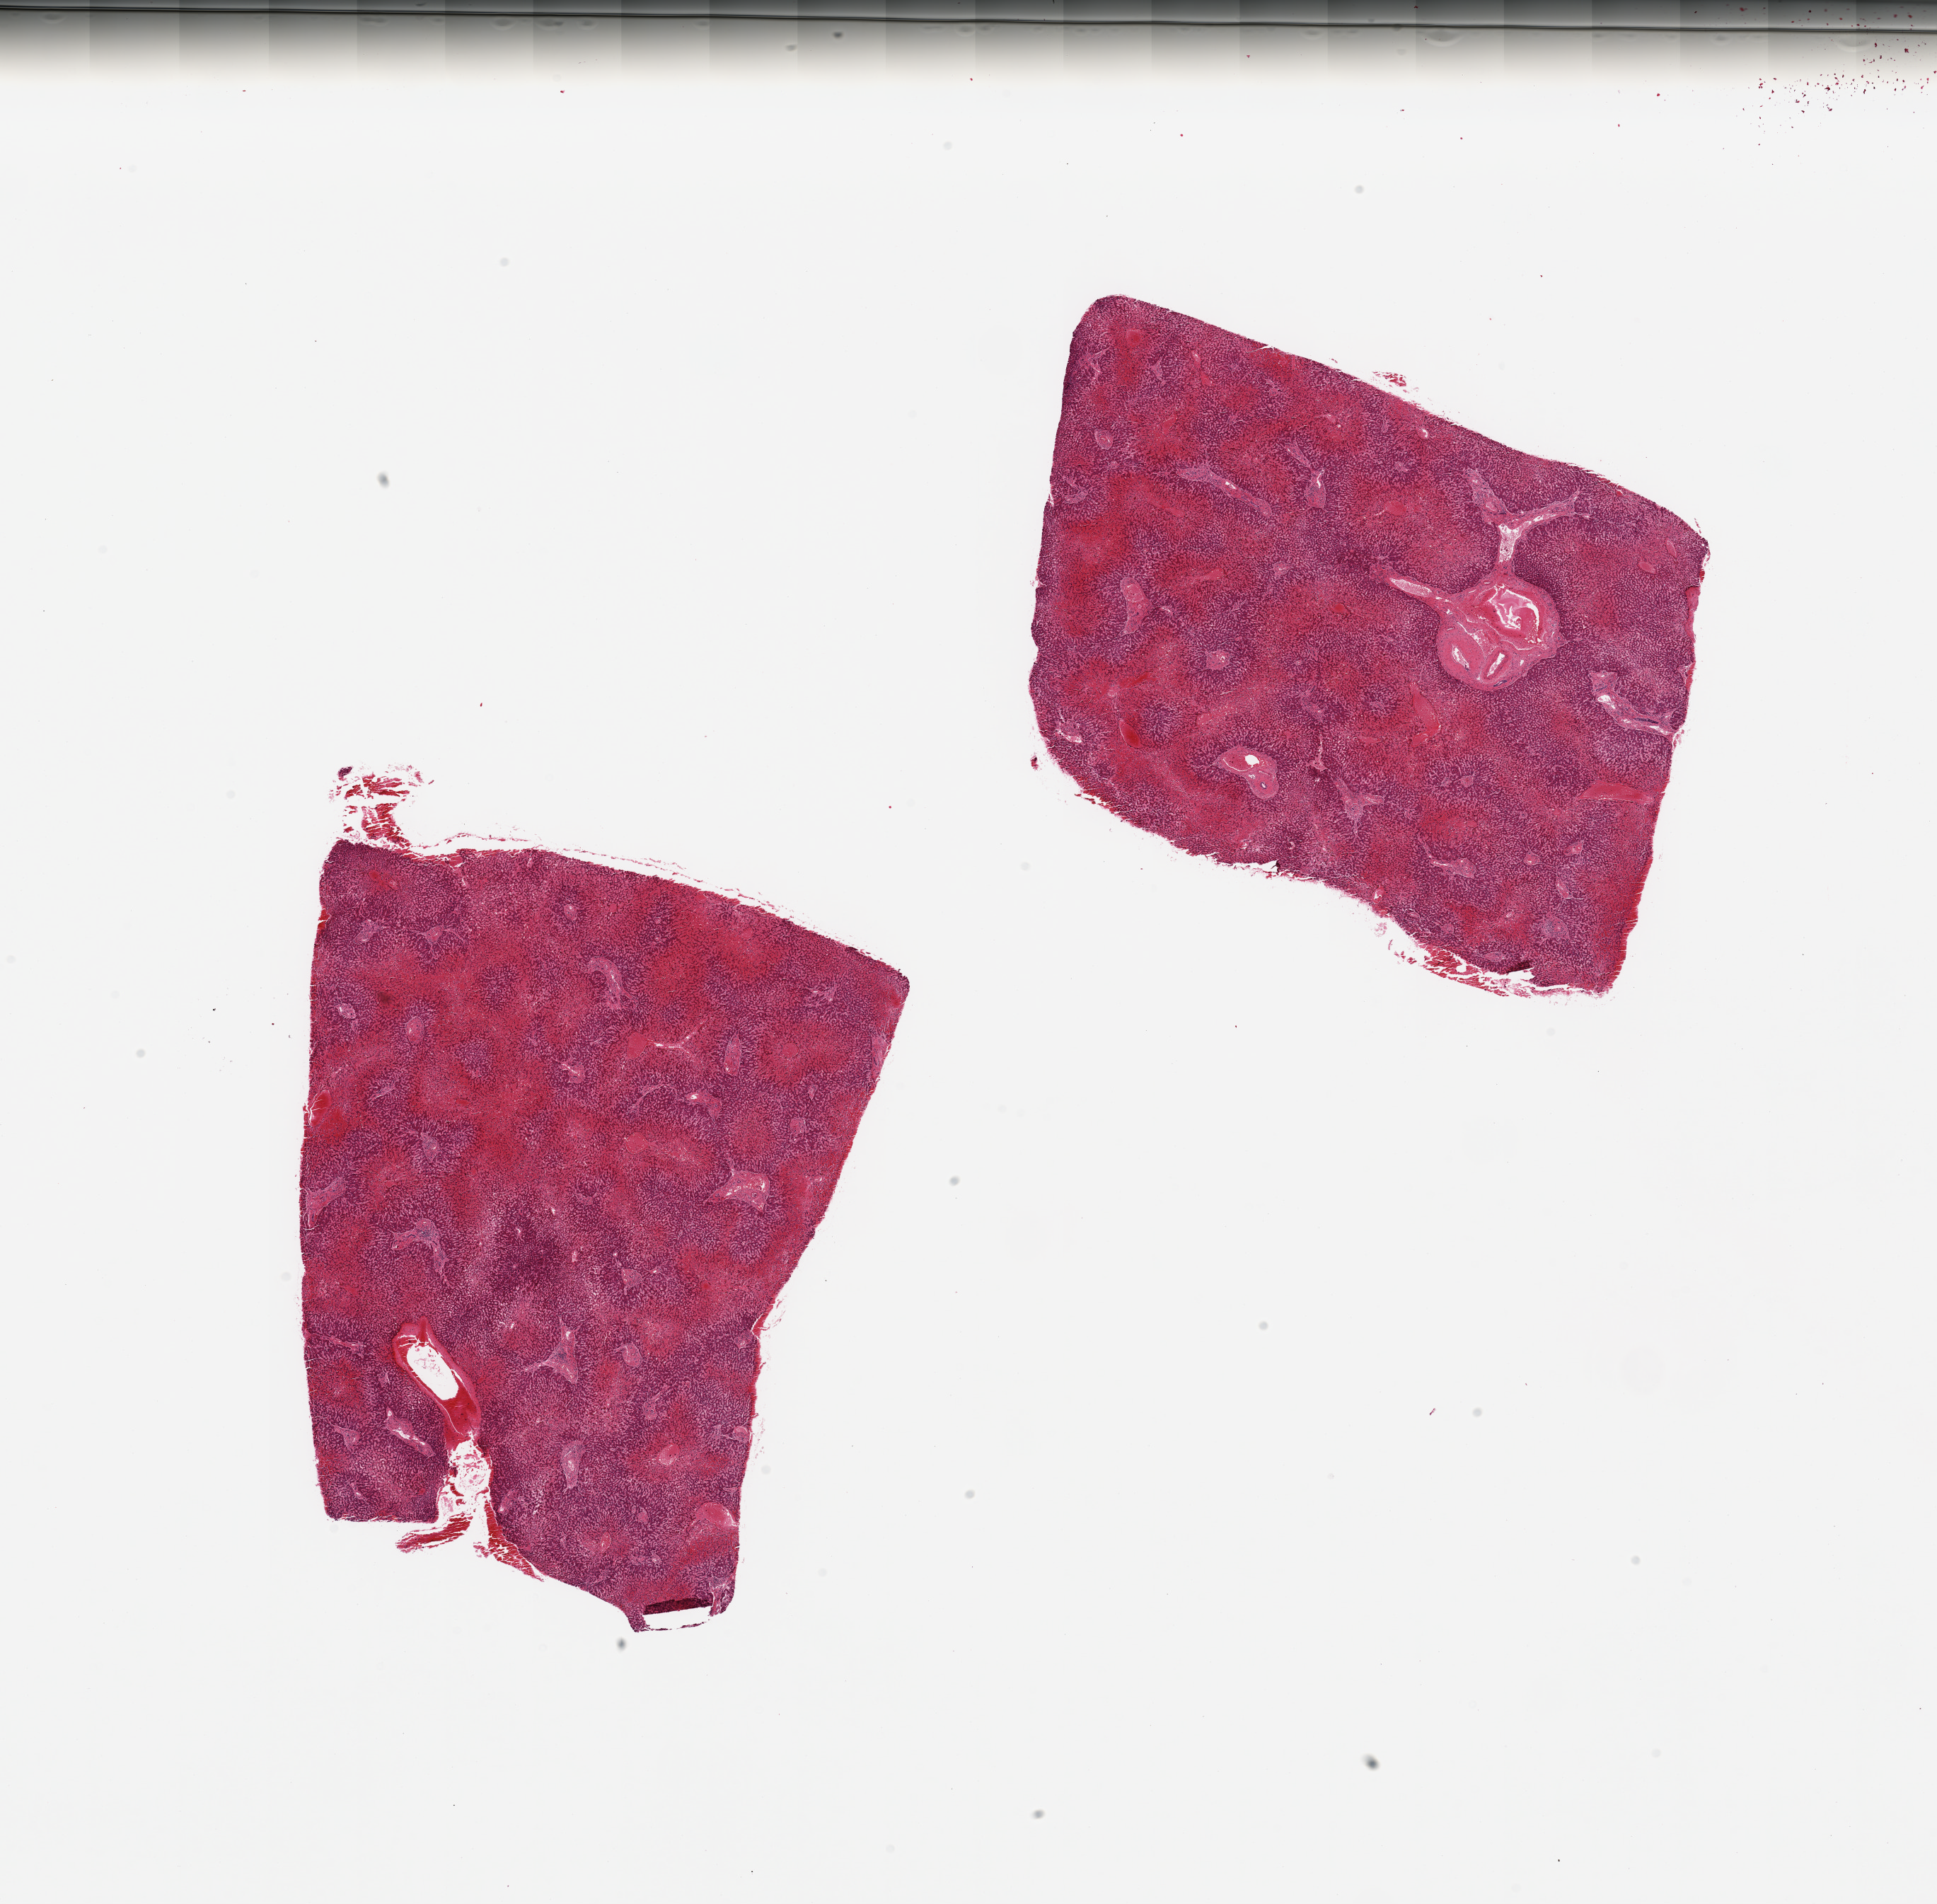
H&E whole-slide image — low-resolution overview of the scanned area, about 21.7 x 21.3 mm (acquisition: 20x scan); PAXgene-fixed paraffin-embedded (PFPE) section; section of liver (target tissue); donor tissue sample. Female donor.
Review note (as recorded): 2 pieces, marked subacute central cardiac congestion.